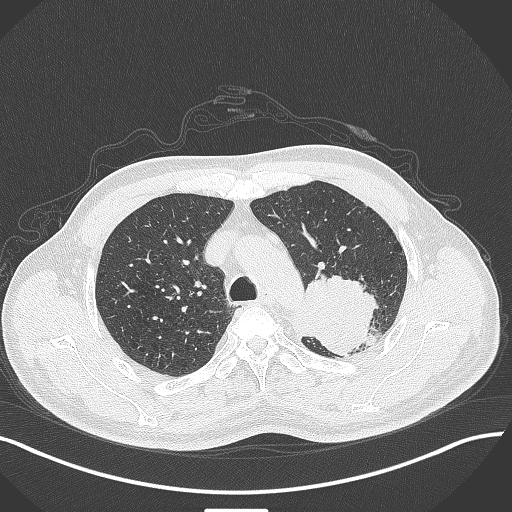
Chest CT, one axial slice; position 320 of 429 along the scan axis; lung window (W 1500 / L -600 HU); 1 mm slice thickness; 512 × 512 image matrix, field of view 400 × 400 mm. Patient: male, 55 years. From the clinical record (not read from this slice): clinical TNM (as recorded): T3 N0 M1c; histopathological grade: G3.
Structures marked on this image (rectangle marked by the reading radiologist):
- lung tumour (recorded histology: adenocarcinoma): box from (x=287, y=264) to (x=384, y=354) px